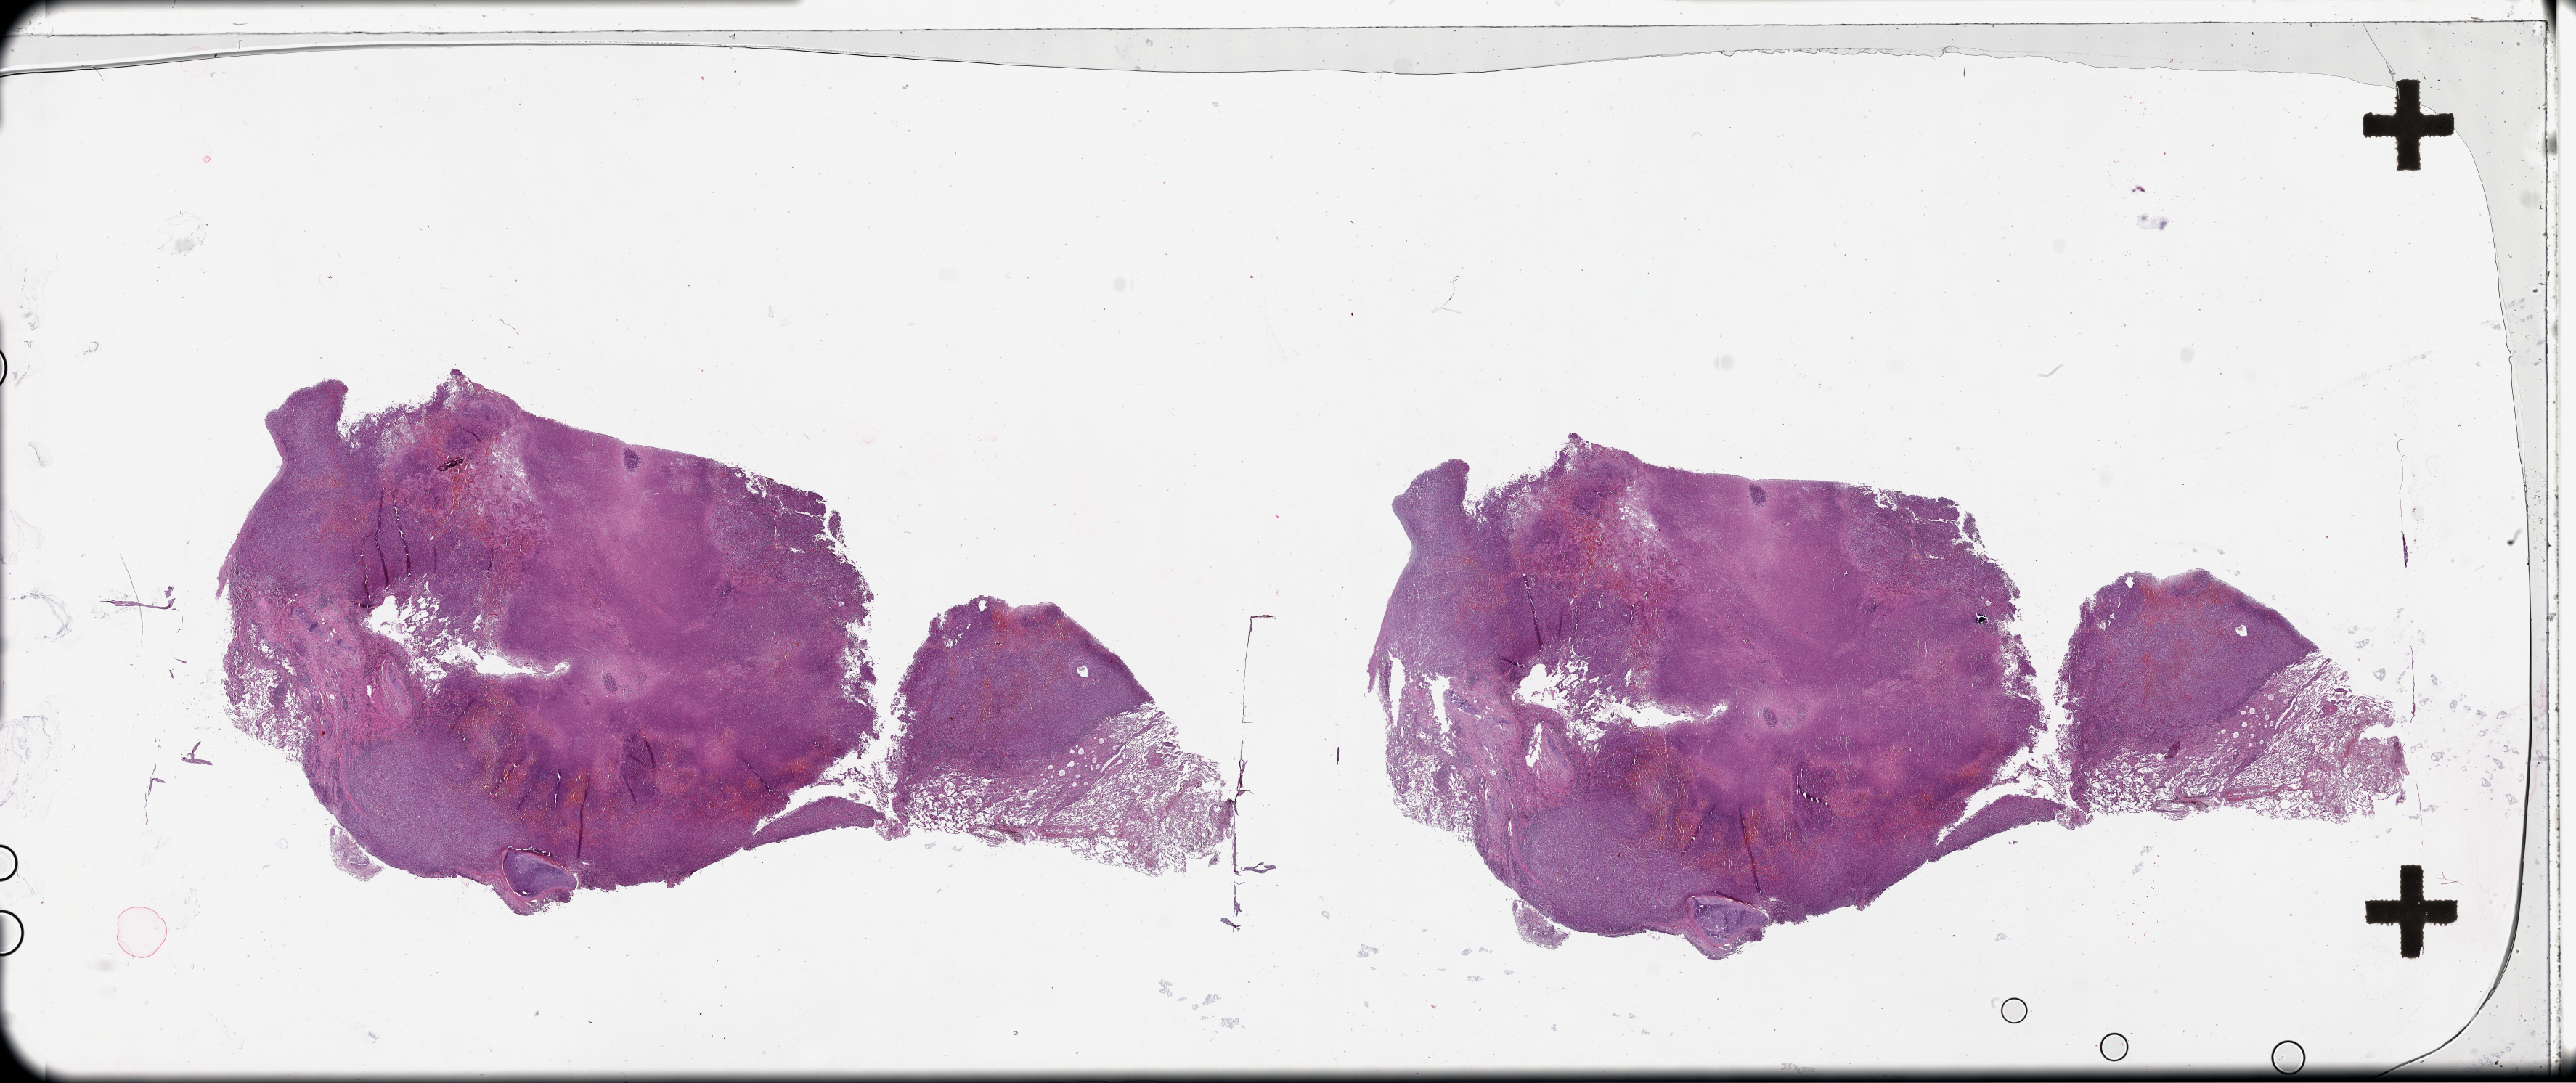
Digitized H&E tissue section (whole slide) — low-resolution overview of the scanned area, about 57.1 x 24.0 mm, tumour tissue sample, lung. 71-year-old male patient.
Patient diagnosis (cohort enrolment): squamous cell carcinoma (lung).